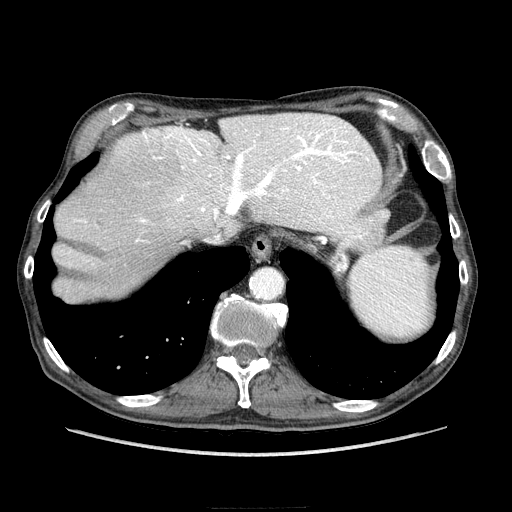
Contrast-enhanced abdominal CT (liver protocol), one axial slice. Slice 183 of 218 in the series (ordered by position). Reconstruction kernel STANDARD. Soft-tissue window (W 400 / L 40 HU). 2.5 mm slice thickness. 512 × 512 image matrix. From the clinical record (not read from this slice): diagnosis: hepatocellular carcinoma (patient treated with transarterial chemoembolisation; whether this scan precedes or follows treatment is not stated here); TNM stage (as recorded): Stage-IIIA; Child-Pugh class: A; tumour differentiation: well differentiated; tumour nodularity: multinodular.
Structures marked on this image (semi-automatic segmentation, software-assisted and operator-edited):
- liver parenchyma outside the tumour (the mass and vessels are separate outlines, so this box may not span the whole liver): box from (x=56, y=114) to (x=380, y=294) px
- liver vessels: (x=74, y=114)–(x=377, y=265)